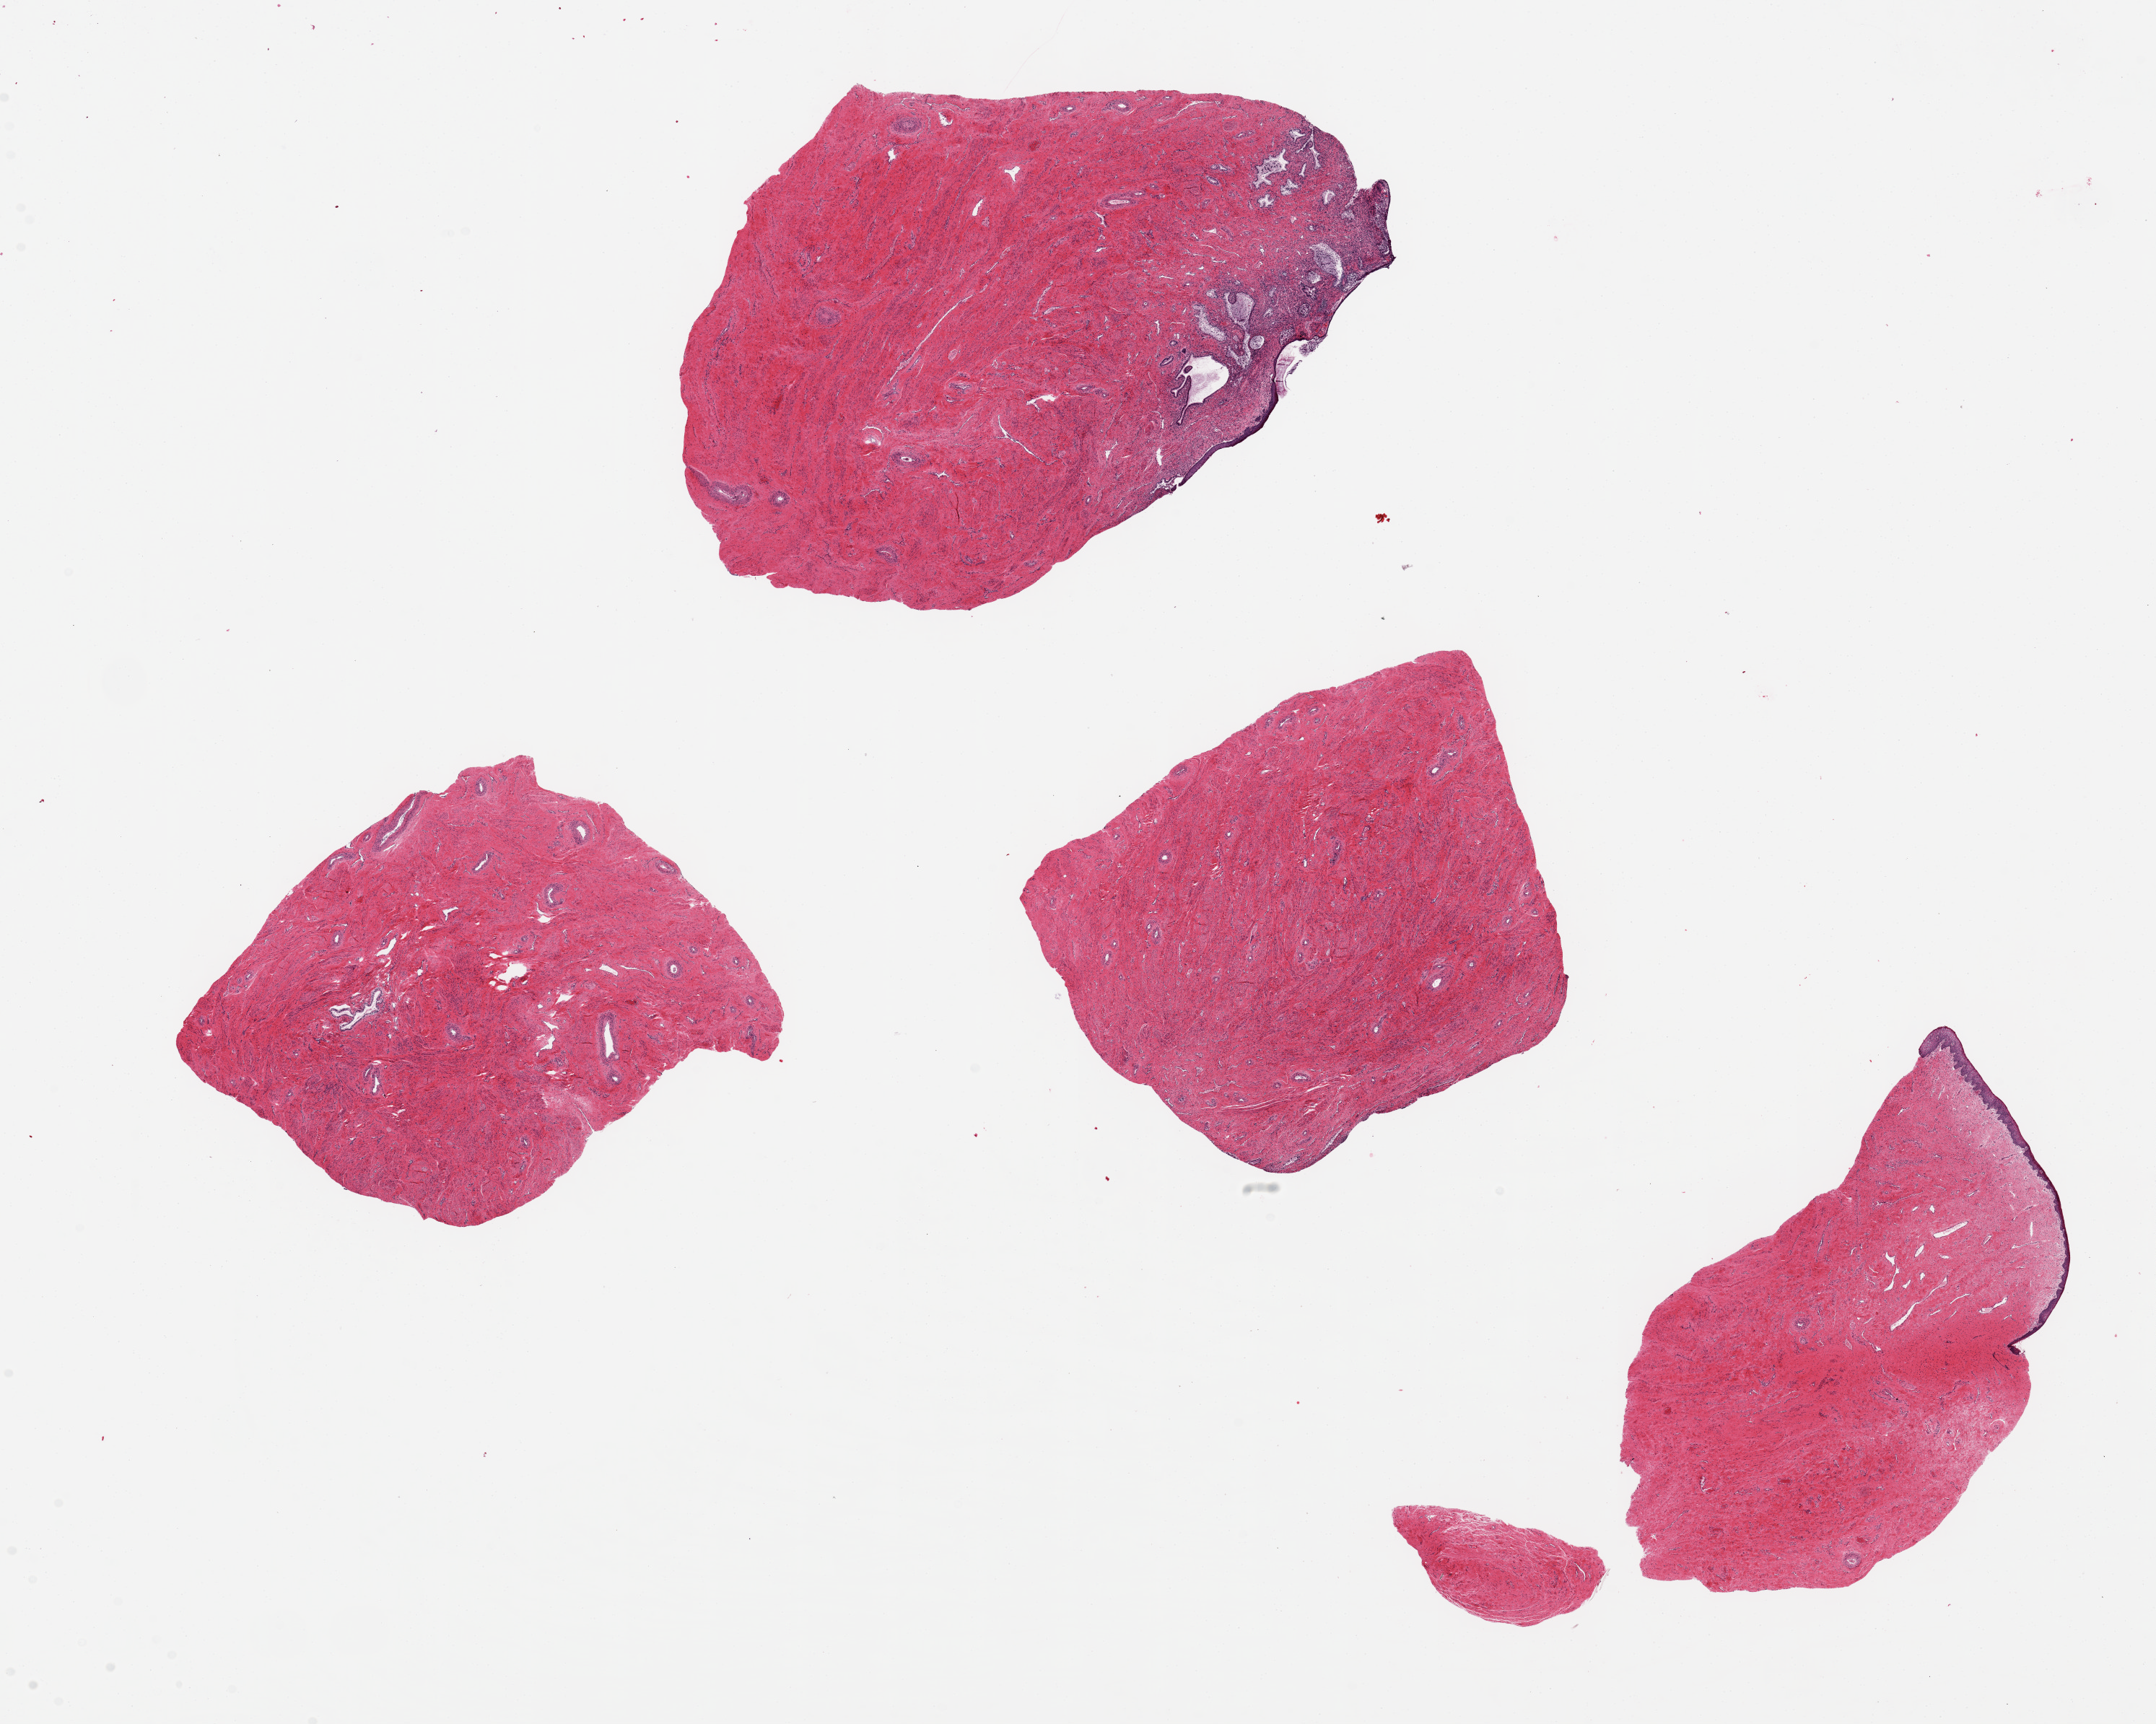
Whole-slide image, haematoxylin and eosin stain, low-resolution overview of the scanned area, about 23.6 x 18.9 mm. PAXgene-fixed paraffin-embedded (PFPE) section. Sampled site (target tissue): endocervix. Donor tissue sample.
- reviewer comment on this tissue sample: 4 ~6x5mm pieces. Only one has a ~3x2mm focus of endocervical glands, partially autolyzed. One has a 3x0.1mm edge of squamous mucosa; the other two lack a mucosal surface